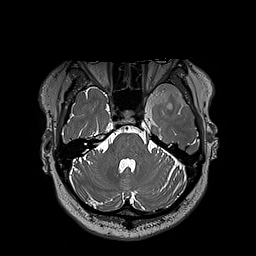
Brain MRI from a brain-tumour surgery series, one axial slice; position 145 of 192 along the scan axis; 1 mm slice thickness; 256 × 256 image matrix, field of view 250 × 250 mm. Case-level facts recorded for this patient, not image findings: histopathology: Oligodendroglioma; WHO grade: 3; IDH mutation: yes.
Structures marked on this image (manually delineated by an expert):
- tumour: bounding box <152,83,192,113> (left, top, right, bottom; pixels)